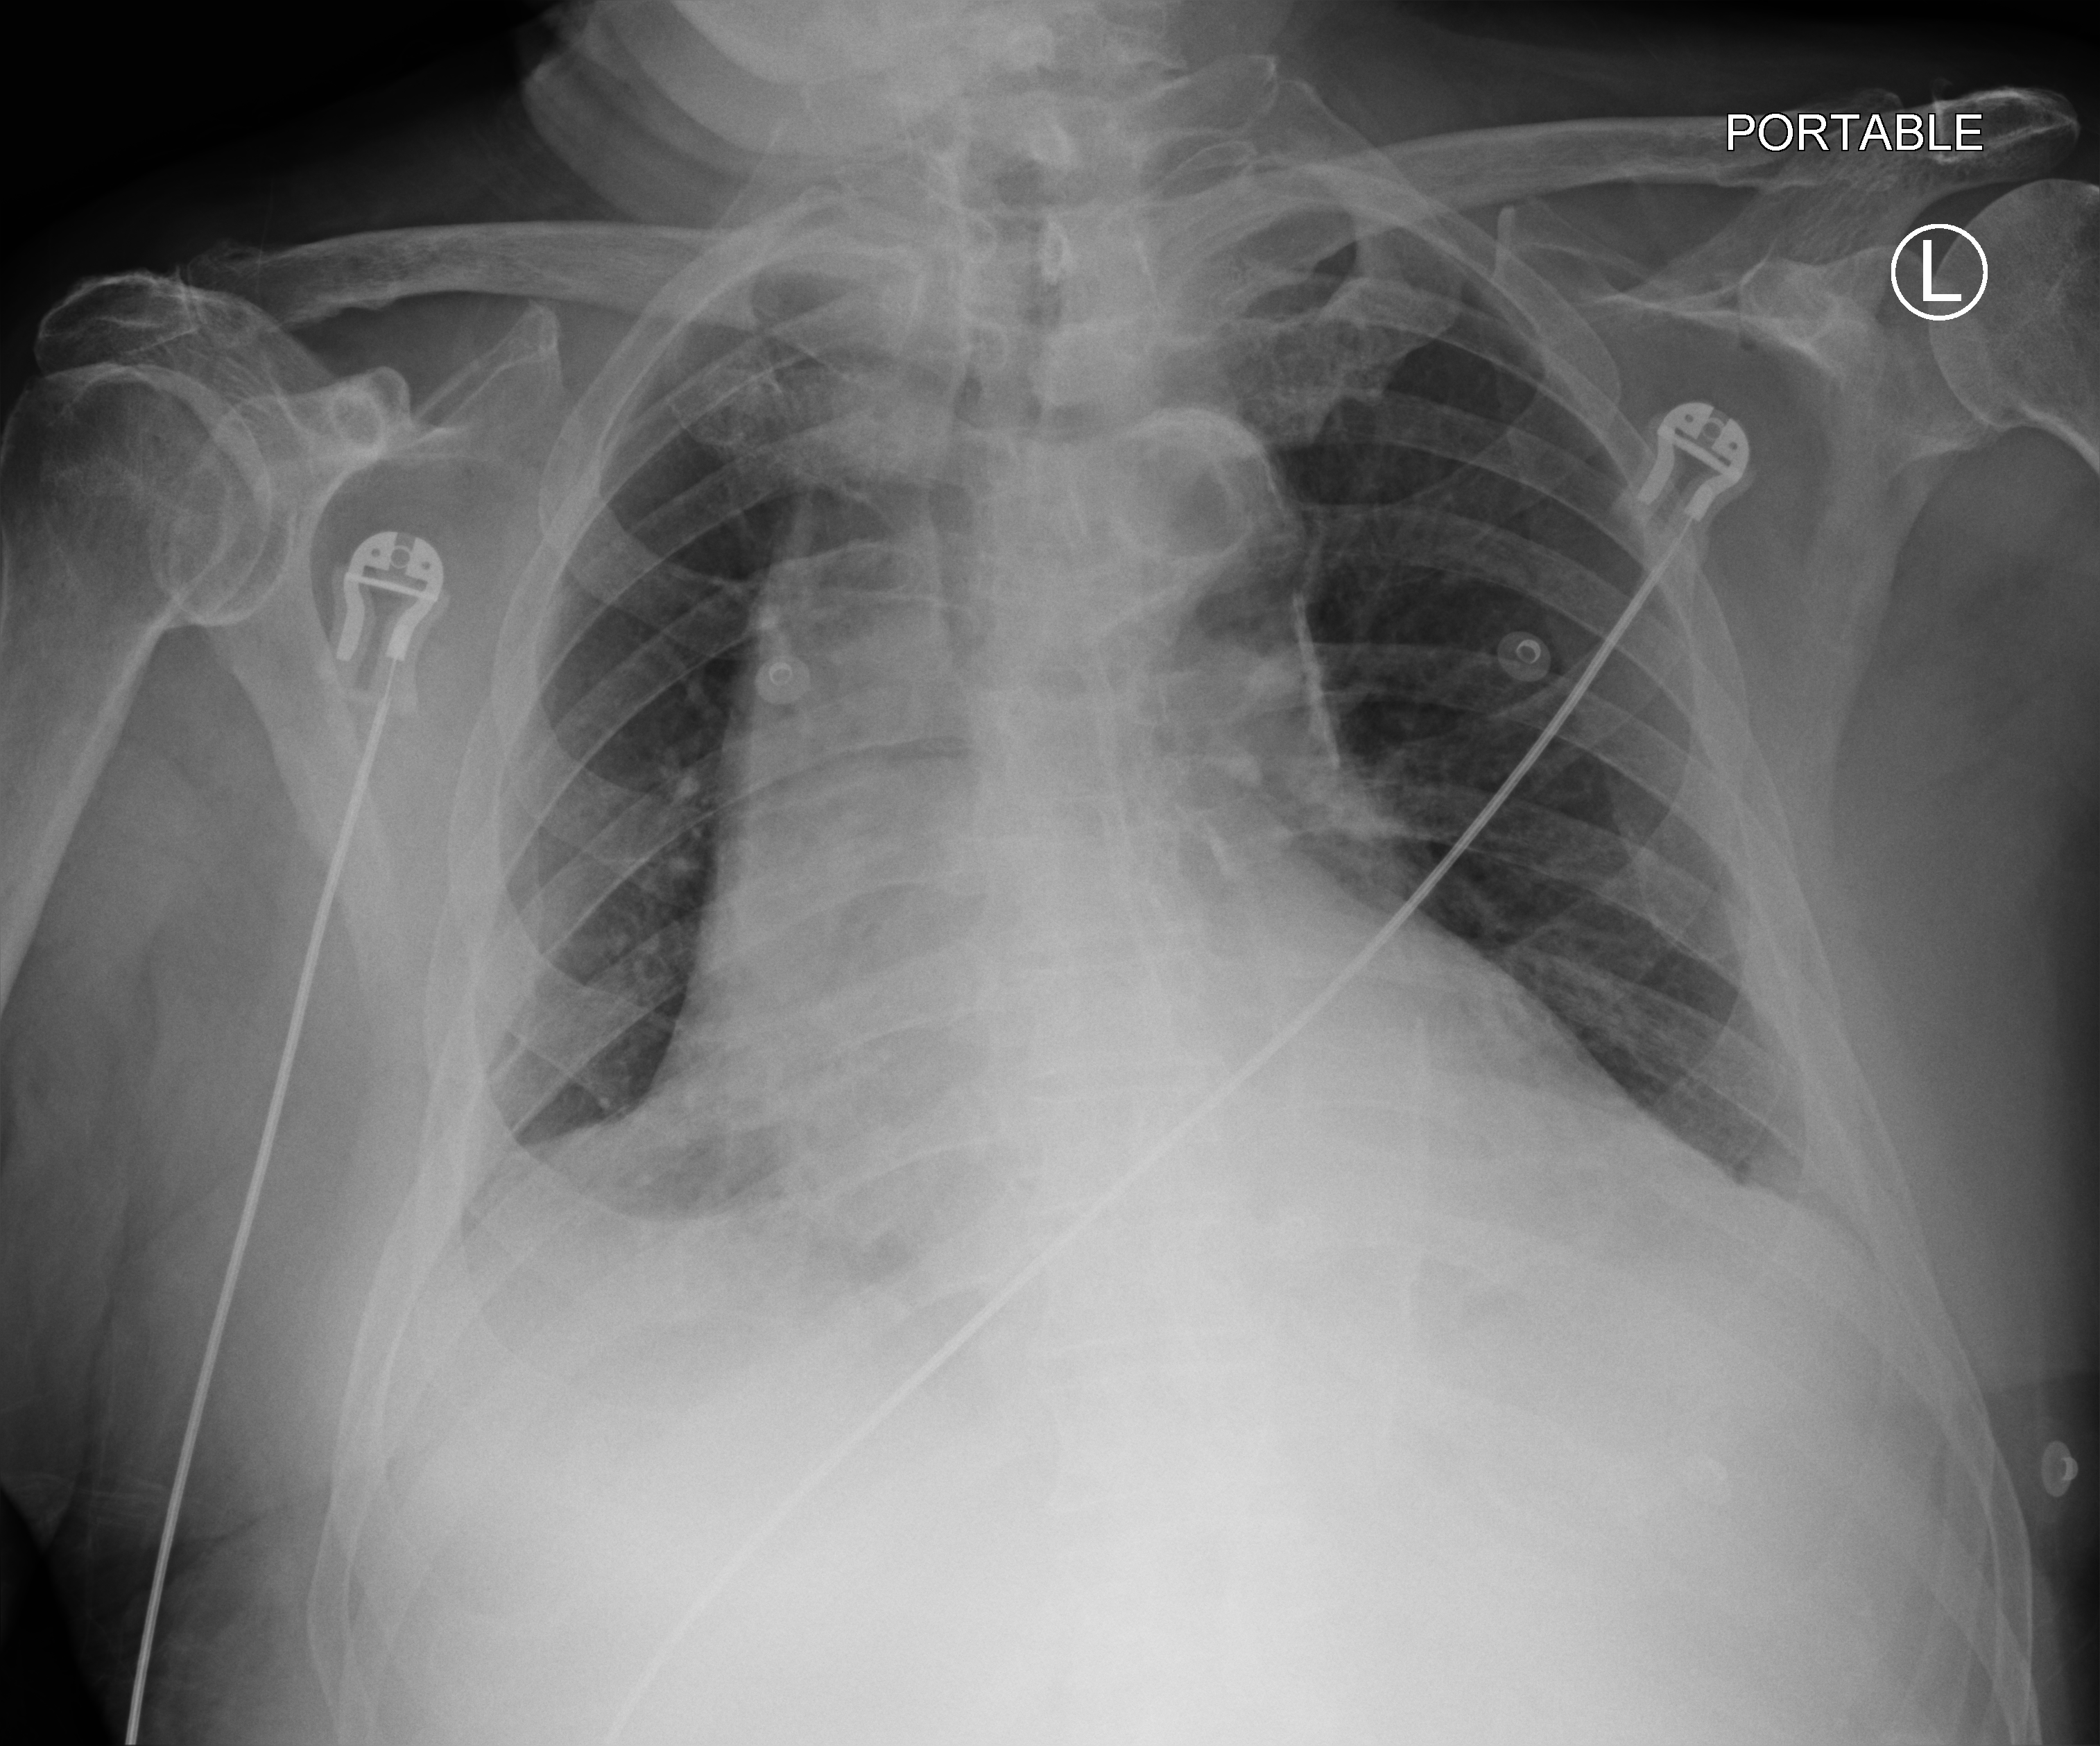
Bedside chest radiograph (computed radiography); anteroposterior (AP) projection. Male patient hospitalised with COVID-19, age 75–90 years.
Admission-level facts for this patient (not findings on this image; timing relative to this image not recorded):
- diabetes (admission record): no
- chronic kidney disease (admission record): yes
- smoking status (admission record): former